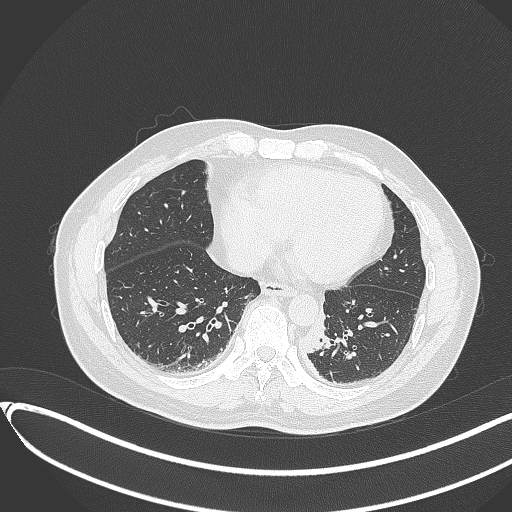
Chest CT, one axial slice. Slice 105 of 417 in the series (ordered by position). Reconstruction kernel B70f. 120 kVp. Lung window (W 1500 / L -600 HU). 1 mm slice thickness. 512 × 512 image matrix, field of view 400 × 400 mm. Patient: male, 54 years. Case-level facts recorded for this patient, not image findings: clinical TNM (as recorded): T3 N0 M0.
Annotated regions visible in this slice (rectangle marked by the reading radiologist):
- lung tumour (recorded histology: squamous cell carcinoma): bounding box [x1, y1, x2, y2] px = [297, 292, 330, 356]